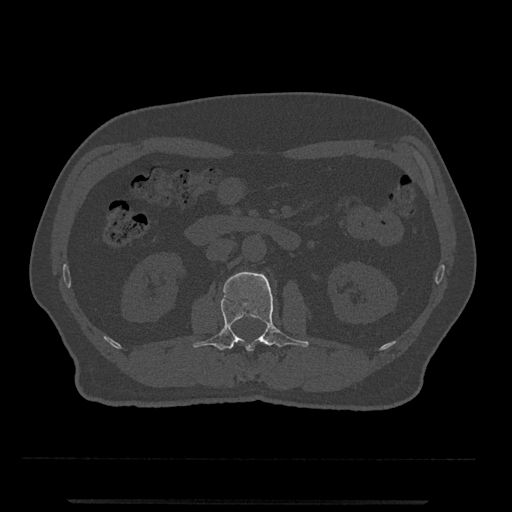
CT including the spine, one axial slice. Slice 273 of 797 in the series (ordered by position). Reconstruction kernel Br40s/3. 120 kVp. Bone window (W 1800 / L 400 HU). 0.5 mm slice thickness. 512 × 512 image matrix. Patient: male, 63 years. Case-level facts recorded for this patient, not image findings: primary cancer: prostate.
Outlined on this slice (semi-automatic segmentation, software-assisted and operator-edited):
- L2 vertebra: box from (x=193, y=272) to (x=309, y=351) px